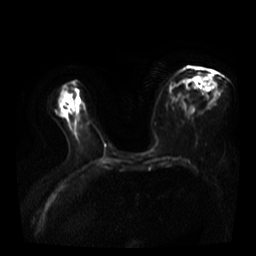
Breast MRI, one axial slice; slice 21 of 40 in the series (ordered by position); diffusion-weighted series; image 2 of 4 stored at this slice position (different b-values; order by instance number); 3 T; 5 mm slice thickness; 256 × 256 image matrix, field of view 360 × 360 mm. Female patient.
Outlined on this slice (outlined manually by an expert reader):
- tumour on diffusion-weighted imaging: bounding box (x1, y1, x2, y2) in pixels: (202, 74, 210, 79)